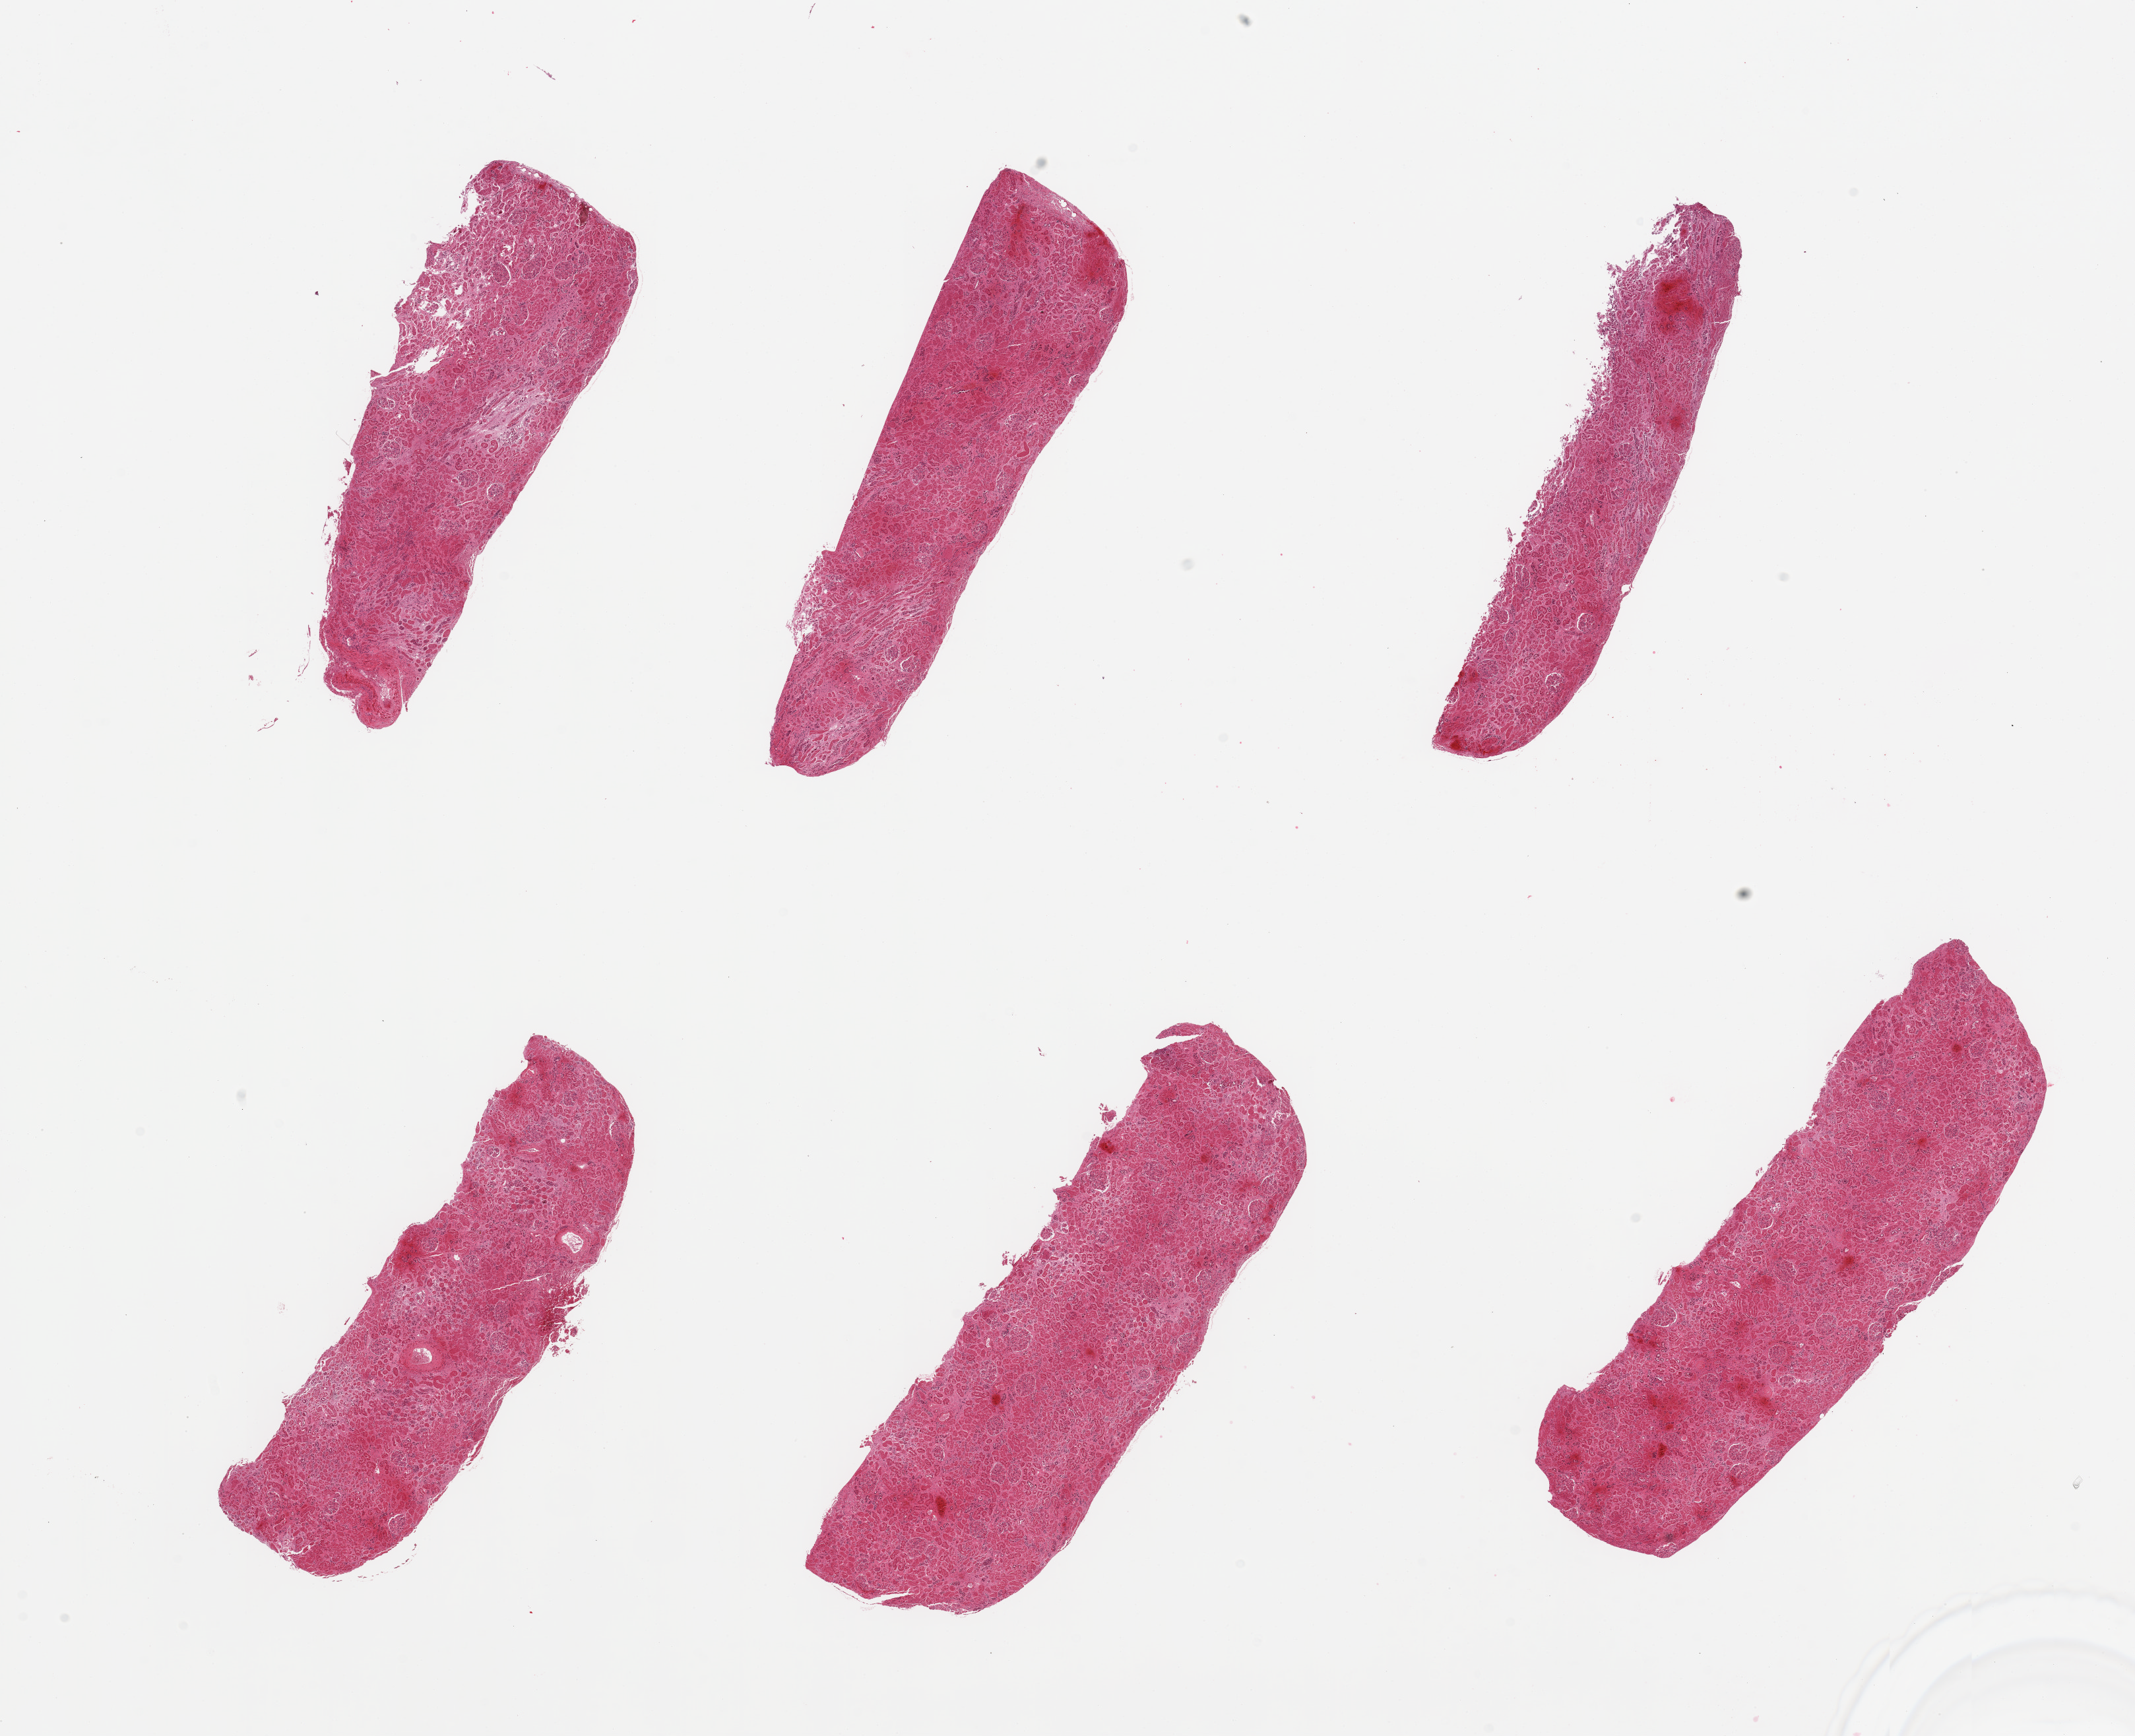
Digitized H&E-stained section — a low-resolution overview of the entire scanned area, about 25.6 x 20.8 mm, PAXgene-fixed, paraffin-embedded tissue, sampled site (target tissue): renal cortex, tissue donor sample. Donor sex: female.
* pathologist's review note for this sample: 6 pieces; no sign of active or chronic lesions